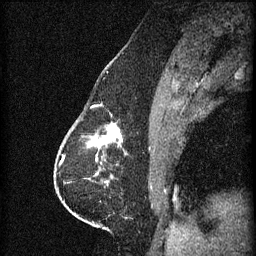
Breast MRI (dynamic contrast-enhanced), one sagittal slice; slice 25 of 60 in the series (ordered by position); 3 images stored at this slice position (order not interpretable as contrast timing); 1.5 T; TE 4.2 ms, TR 11 ms; 1.5 mm slice thickness; 256 × 256 image matrix, field of view 180 × 180 mm. Patient: female, 63 years.
Annotated regions visible in this slice (semi-automatic segmentation, software-assisted and operator-edited):
- analysis volume of interest (the breast-tissue region the enhancement analysis was run in; not a lesion): box from (x=86, y=122) to (x=127, y=153) px
- tumour enhancement mask (voxels above the 70 % enhancement threshold inside the analysis volume of interest): (x=88, y=124)–(x=123, y=149)